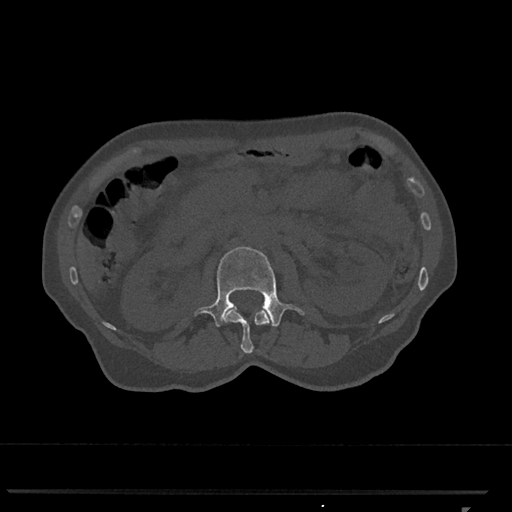
CT including the spine, one axial slice. Position 361 of 793 along the scan axis. 120 kVp. Bone window (W 1800 / L 400 HU). 512 × 512 image matrix. Female patient, age 62 years. From the clinical record (not read from this slice): primary cancer: renal.
Structures marked on this image (semi-automatically segmented with operator editing):
- L1 vertebra: bounding box <223,307,272,354> (left, top, right, bottom; pixels)
- L2 vertebra: <194,247,305,327>